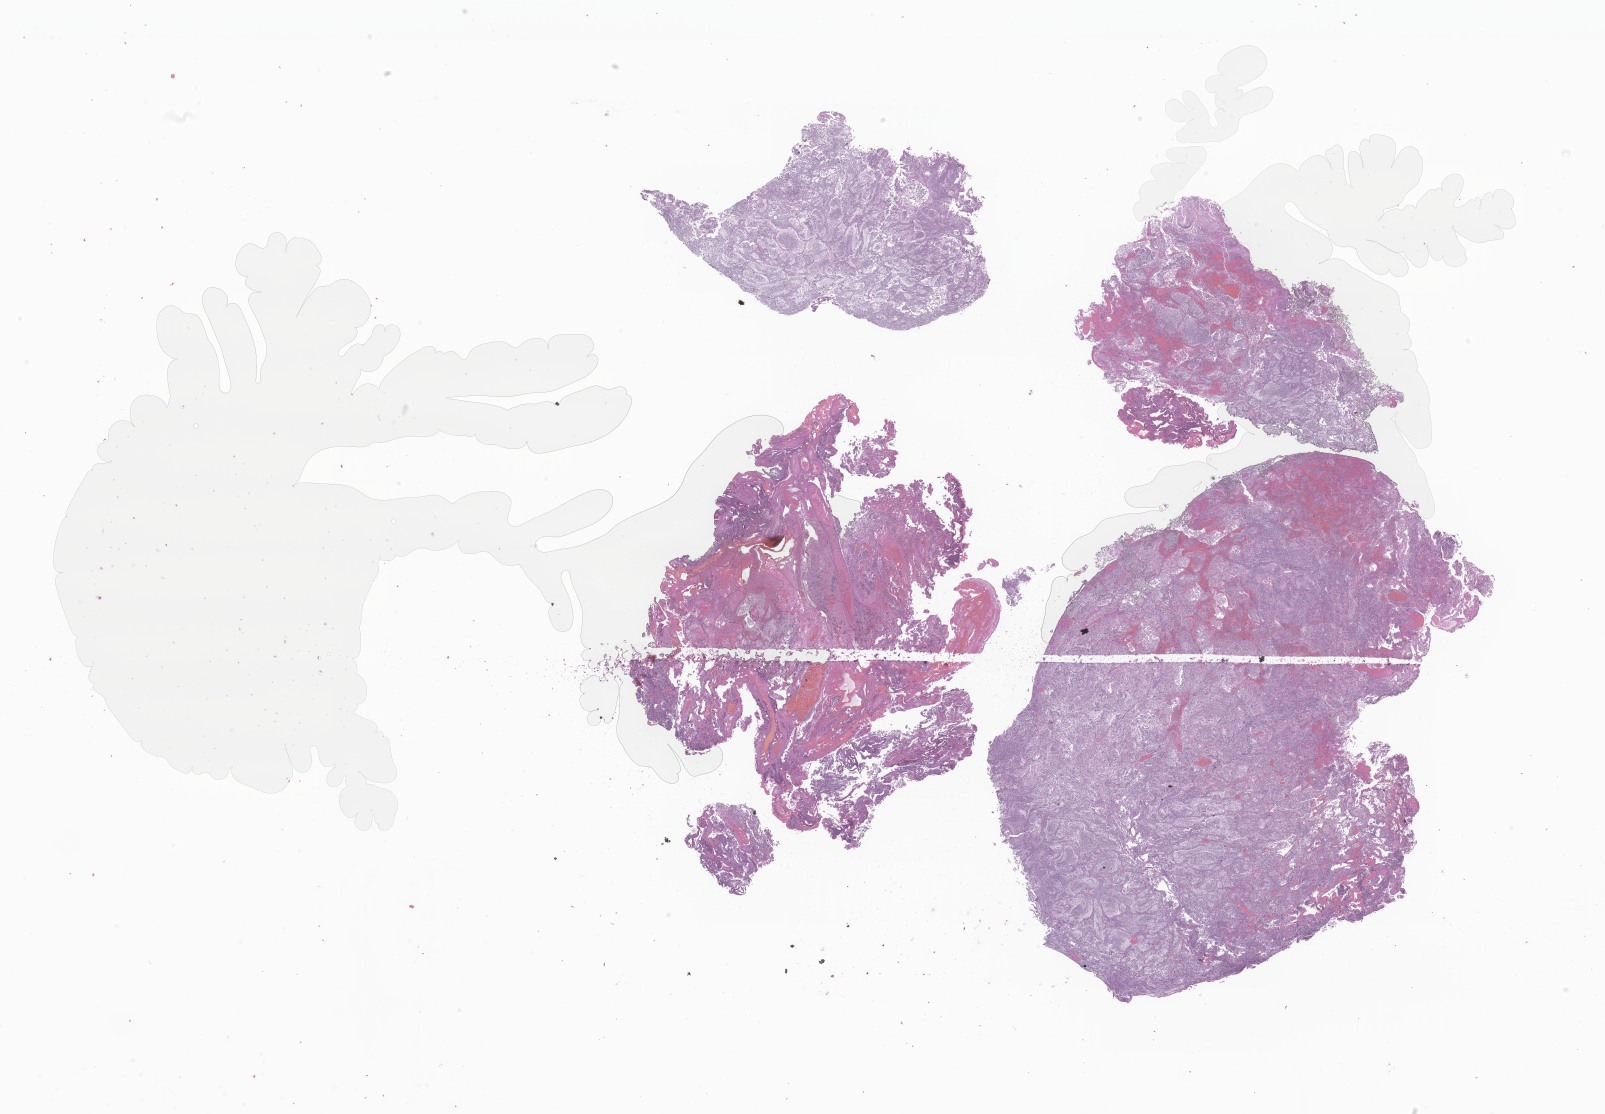
Whole-slide image, hematoxylin and eosin (H&E) stain of tumor tissue from the brain — whole scanned area (about 27.1 x 18.8 mm) shown as a low-resolution overview. Formalin-fixed, paraffin-embedded (FFPE) tissue. Patient male; age 88 days.
Recorded diagnosis: Medulloblastoma, NOS.